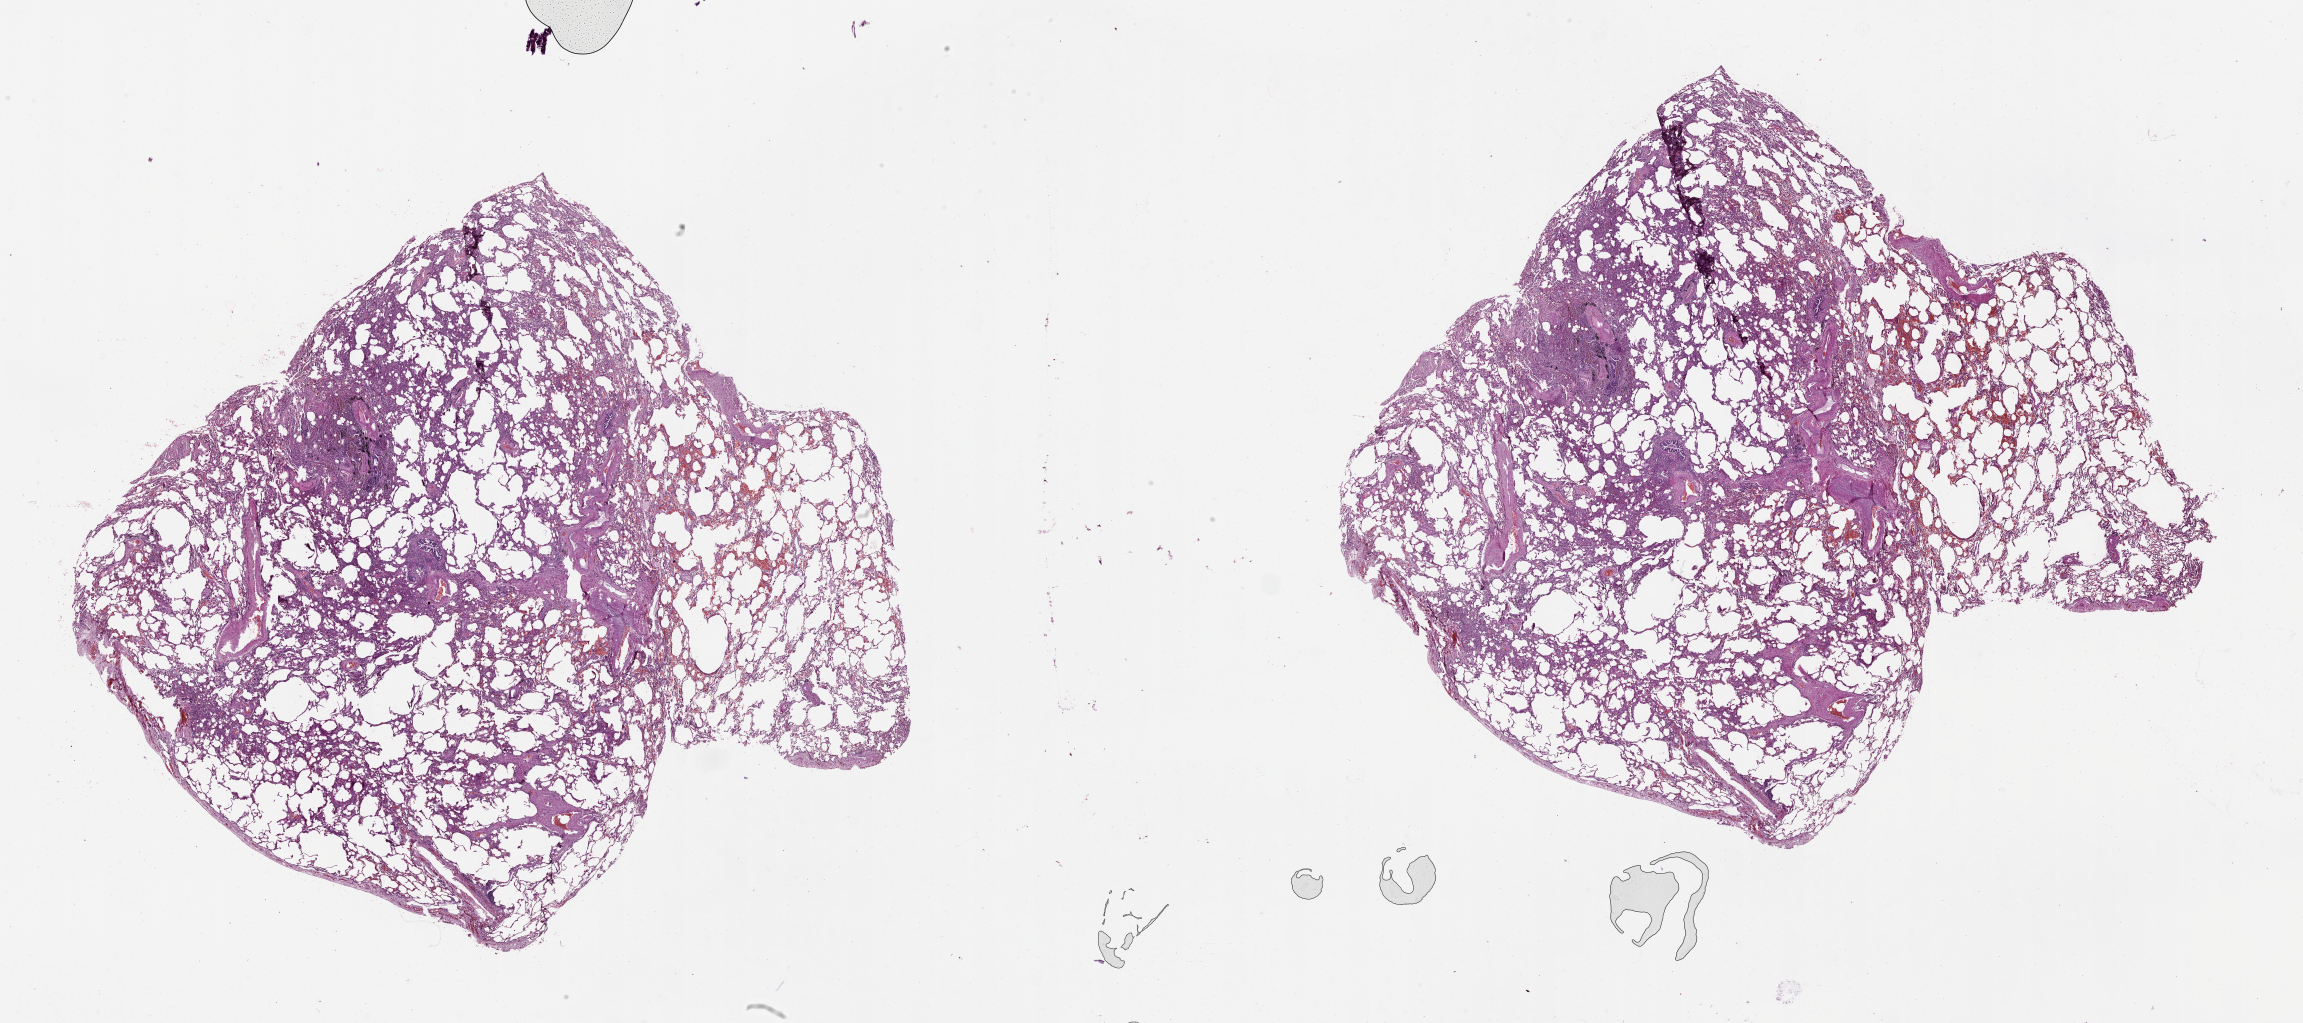
Digitized H&E tissue section (whole slide), shown as a low-resolution overview of the whole scanned area (about 37.1 x 16.5 mm, slide scanned at 20x). Normal (non-tumour) tissue sample, lung. Patient: male, age 53 years.
This section: normal (non-tumour) tissue from the same patient. Patient diagnosis (cohort enrolment): squamous cell carcinoma (lung).